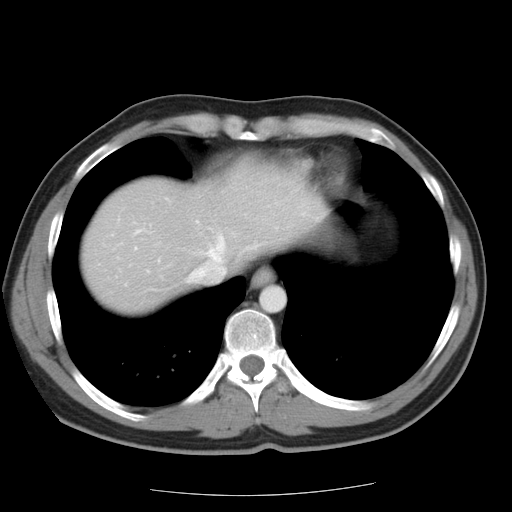
Contrast-enhanced abdominal CT, one axial slice; position 20 of 22 along the scan axis; intravenous contrast given; soft-tissue window (W 400 / L 40 HU); 7.5 mm slice thickness; 512 × 512 image matrix, field of view 359 × 359 mm. Male patient, age 41 years. From the clinical record (not read from this slice): diagnosis: colorectal cancer liver metastases, imaged before liver resection; multiple liver metastases: no; largest metastasis: 2.7 cm; disease in both lobes: no.
Annotated regions visible in this slice (manually delineated by an expert):
- hepatic veins: bounding box (x1, y1, x2, y2) in pixels: (193, 237, 225, 279)
- liver: (84, 167, 310, 307)
- planned liver remnant (the part of the liver to remain after resection): (84, 168, 309, 306)